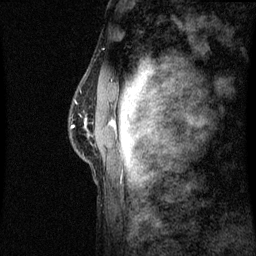
Breast MRI (dynamic contrast-enhanced), one sagittal slice; slice 50 of 60 in the series (ordered by position); dynamic contrast-enhanced series, image 2 of 3 at this slice position (ordered by acquisition); 1.5 T; TE 4.2 ms, TR 8.9 ms; 2 mm slice thickness; 256 × 256 image matrix, field of view 200 × 200 mm. Patient: female, 50 years. Case-level facts recorded for this patient, not image findings: setting: breast cancer imaged before/during neoadjuvant chemotherapy; receptor status: triple-negative.
Annotated regions visible in this slice (semi-automatic segmentation, software-assisted and operator-edited):
- analysis volume of interest (the breast-tissue region the enhancement analysis was run in; not a lesion): box from (x=72, y=80) to (x=116, y=169) px
- tumour enhancement mask (voxels above the 70 % enhancement threshold inside the analysis volume of interest): (x=74, y=122)–(x=116, y=127)